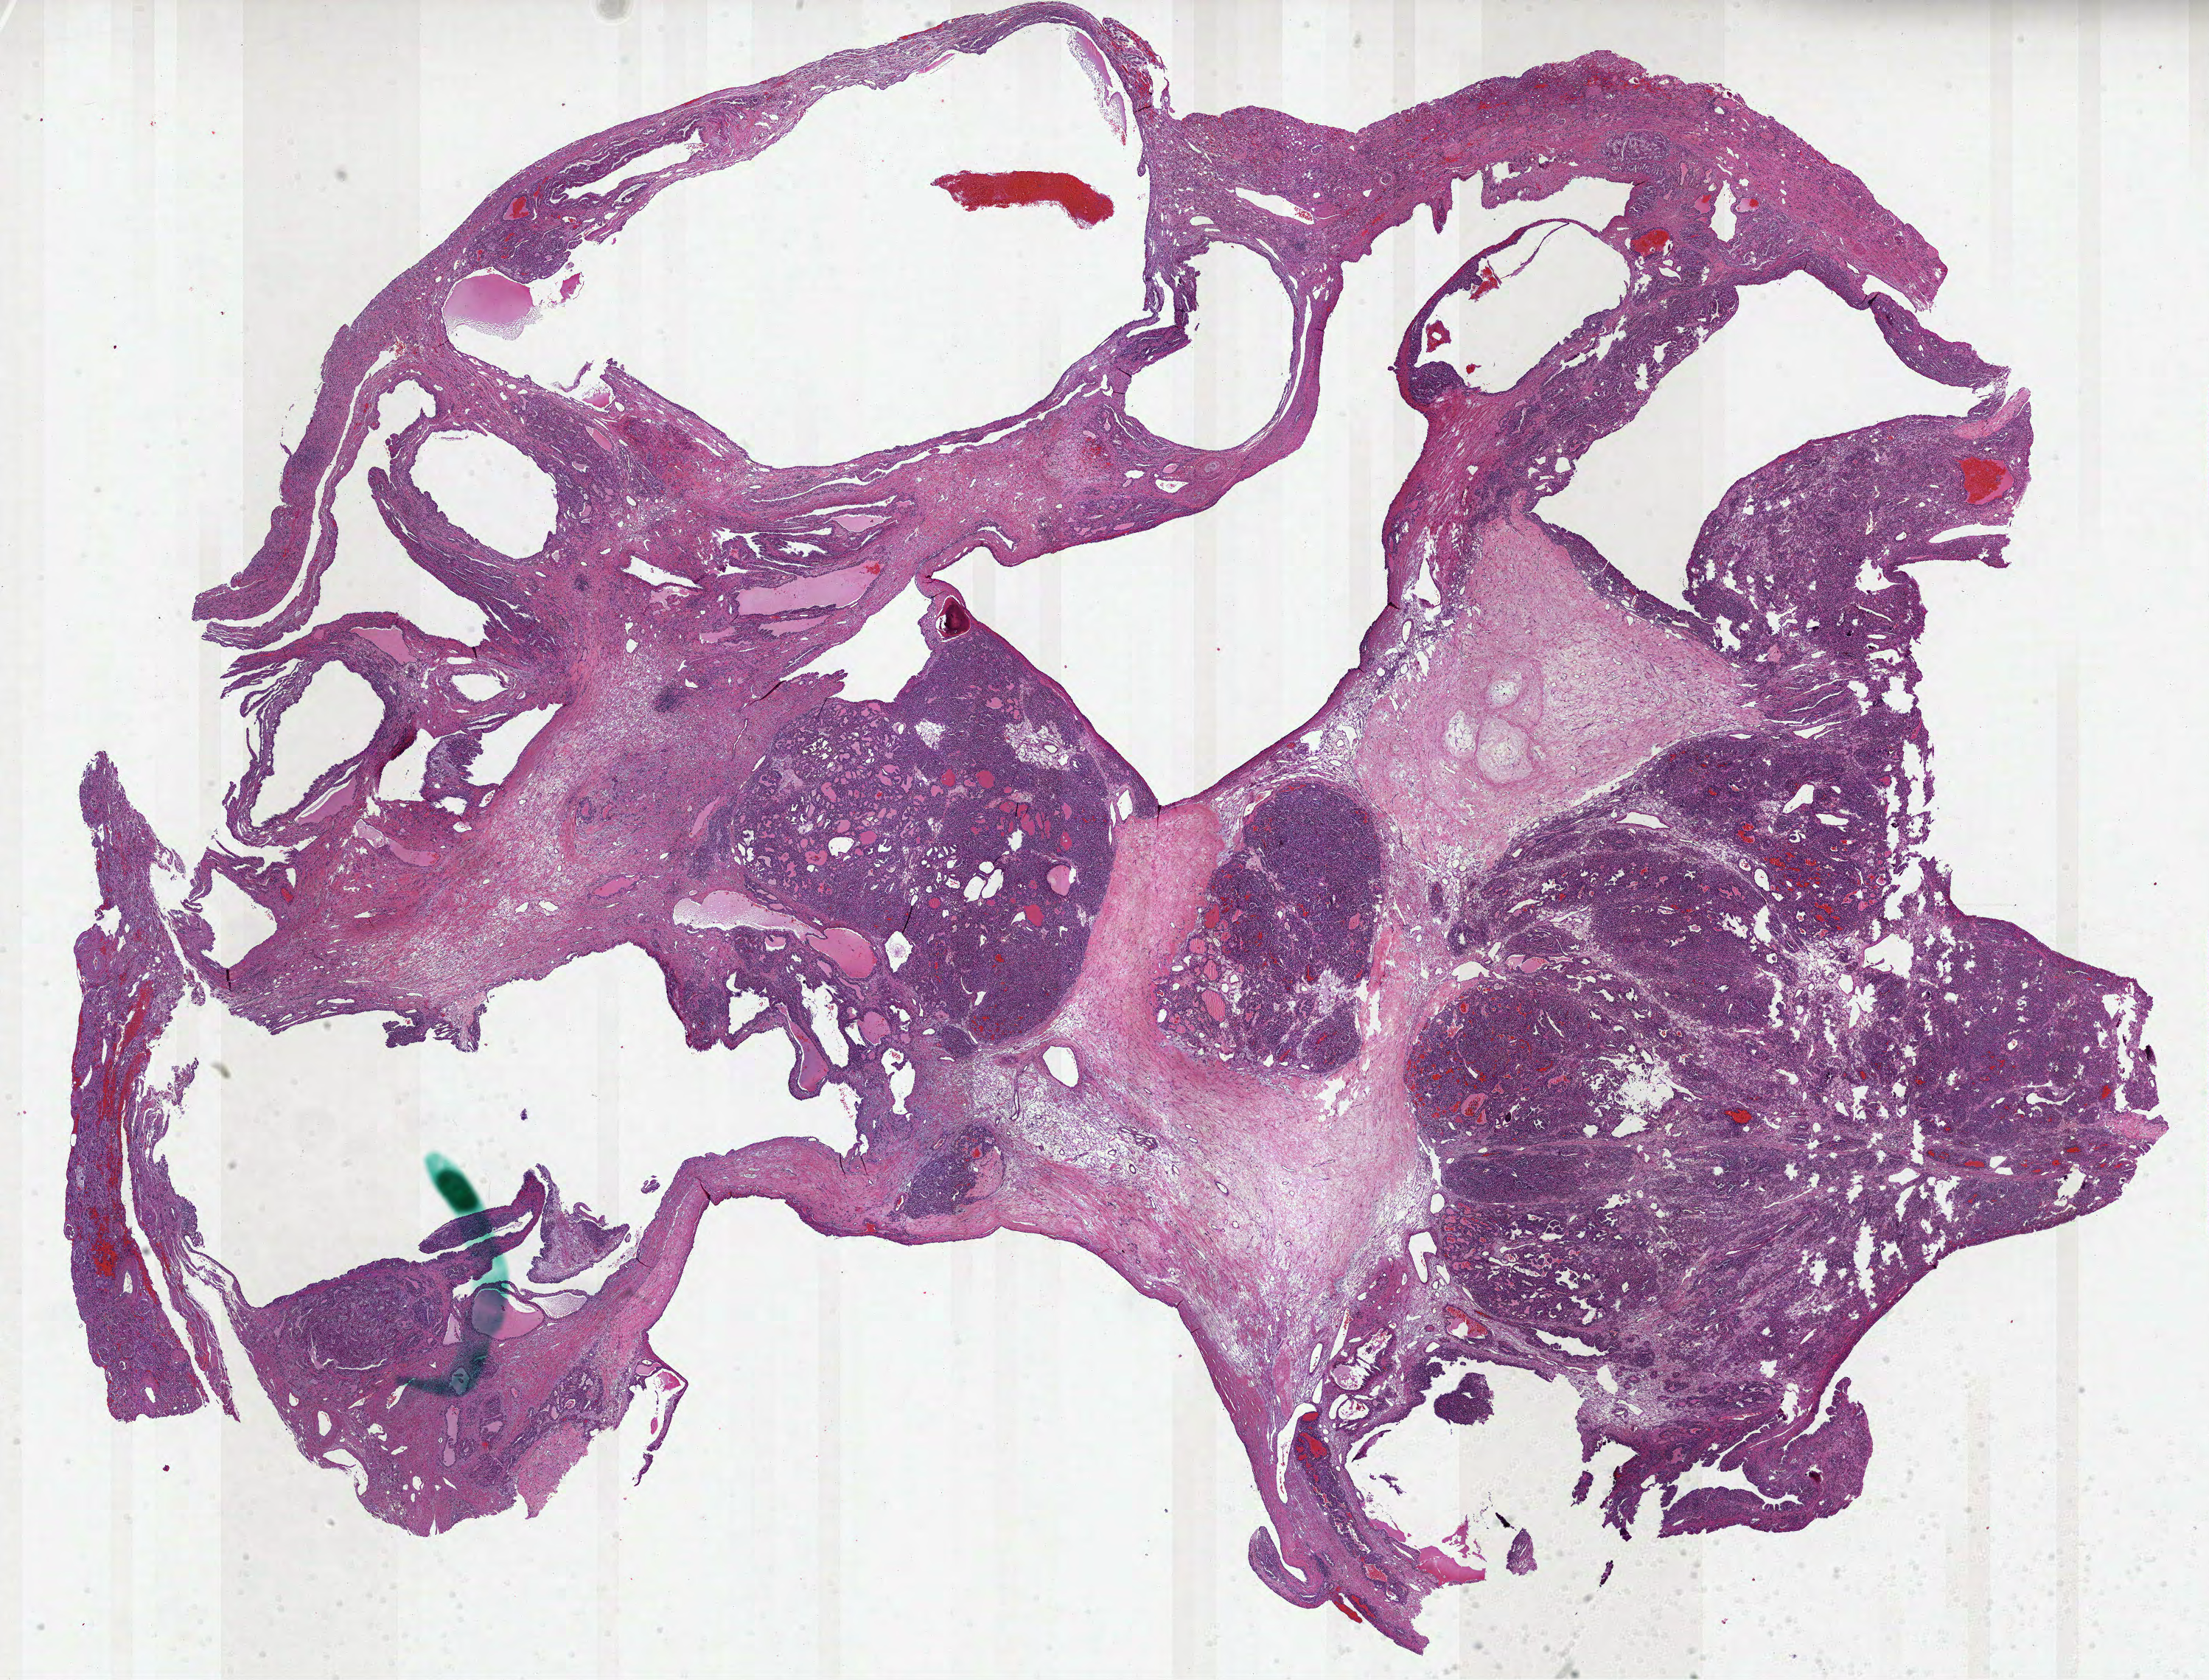
H&E-stained whole-slide image — low-resolution overview of the scanned area, about 24.2 x 18.4 mm. FFPE section. Kidney, primary tumour sample. Female, age 55 years at initial diagnosis. Histologic grade: G2 (moderately differentiated).
- laterality: left
- diagnosis: Clear cell adenocarcinoma, NOS
- AJCC pathologic stage: I